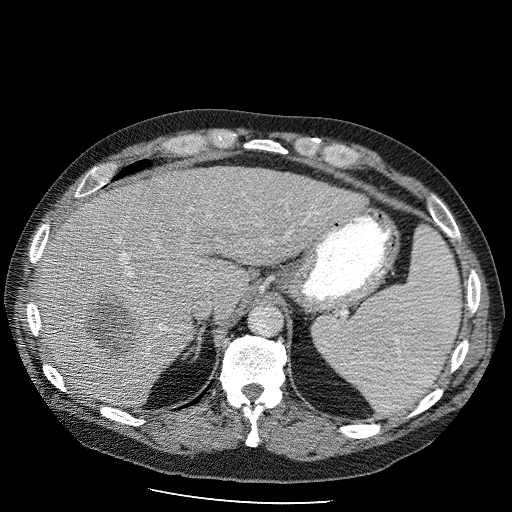
Contrast-enhanced abdominal CT (liver protocol), one axial slice. Position 74 of 98 along the scan axis. Reconstruction kernel STANDARD. Soft-tissue window (W 400 / L 40 HU). 2.5 mm slice thickness. 512 × 512 image matrix. From the clinical record (not read from this slice): diagnosis: hepatocellular carcinoma (patient treated with transarterial chemoembolisation; whether this scan precedes or follows treatment is not stated here); TNM stage (as recorded): Stage-II.
Structures marked on this image (semi-automatic segmentation, software-assisted and operator-edited):
- liver parenchyma outside the tumour (the mass and vessels are separate outlines, so this box may not span the whole liver): bounding box (x1, y1, x2, y2) in pixels: (36, 166, 362, 410)
- mass: (76, 291, 152, 362)
- liver vessels: (126, 194, 239, 321)